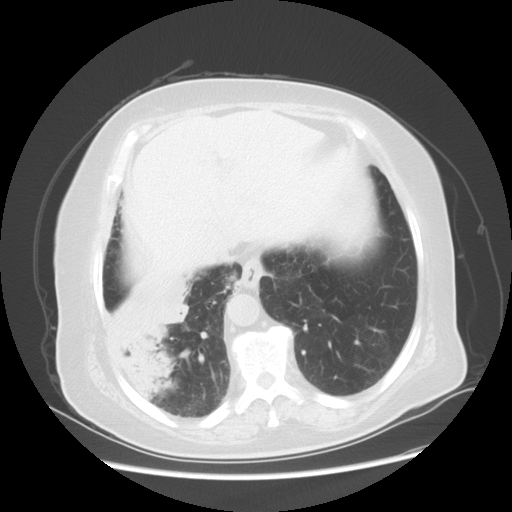
Chest CT, one axial slice. Slice 14 of 56 in the series (ordered by position). Reconstruction kernel STANDARD. 120 kVp. Lung window (W 1500 / L -600 HU). 512 × 512 image matrix, field of view 378 × 378 mm. Patient: female, 73 years. Case-level facts recorded for this patient, not image findings: clinical TNM (as recorded): T3 N0 M0.
Outlined on this slice (rectangle marked by the reading radiologist):
- lung tumour (recorded histology: adenocarcinoma): box from (x=106, y=278) to (x=195, y=407) px